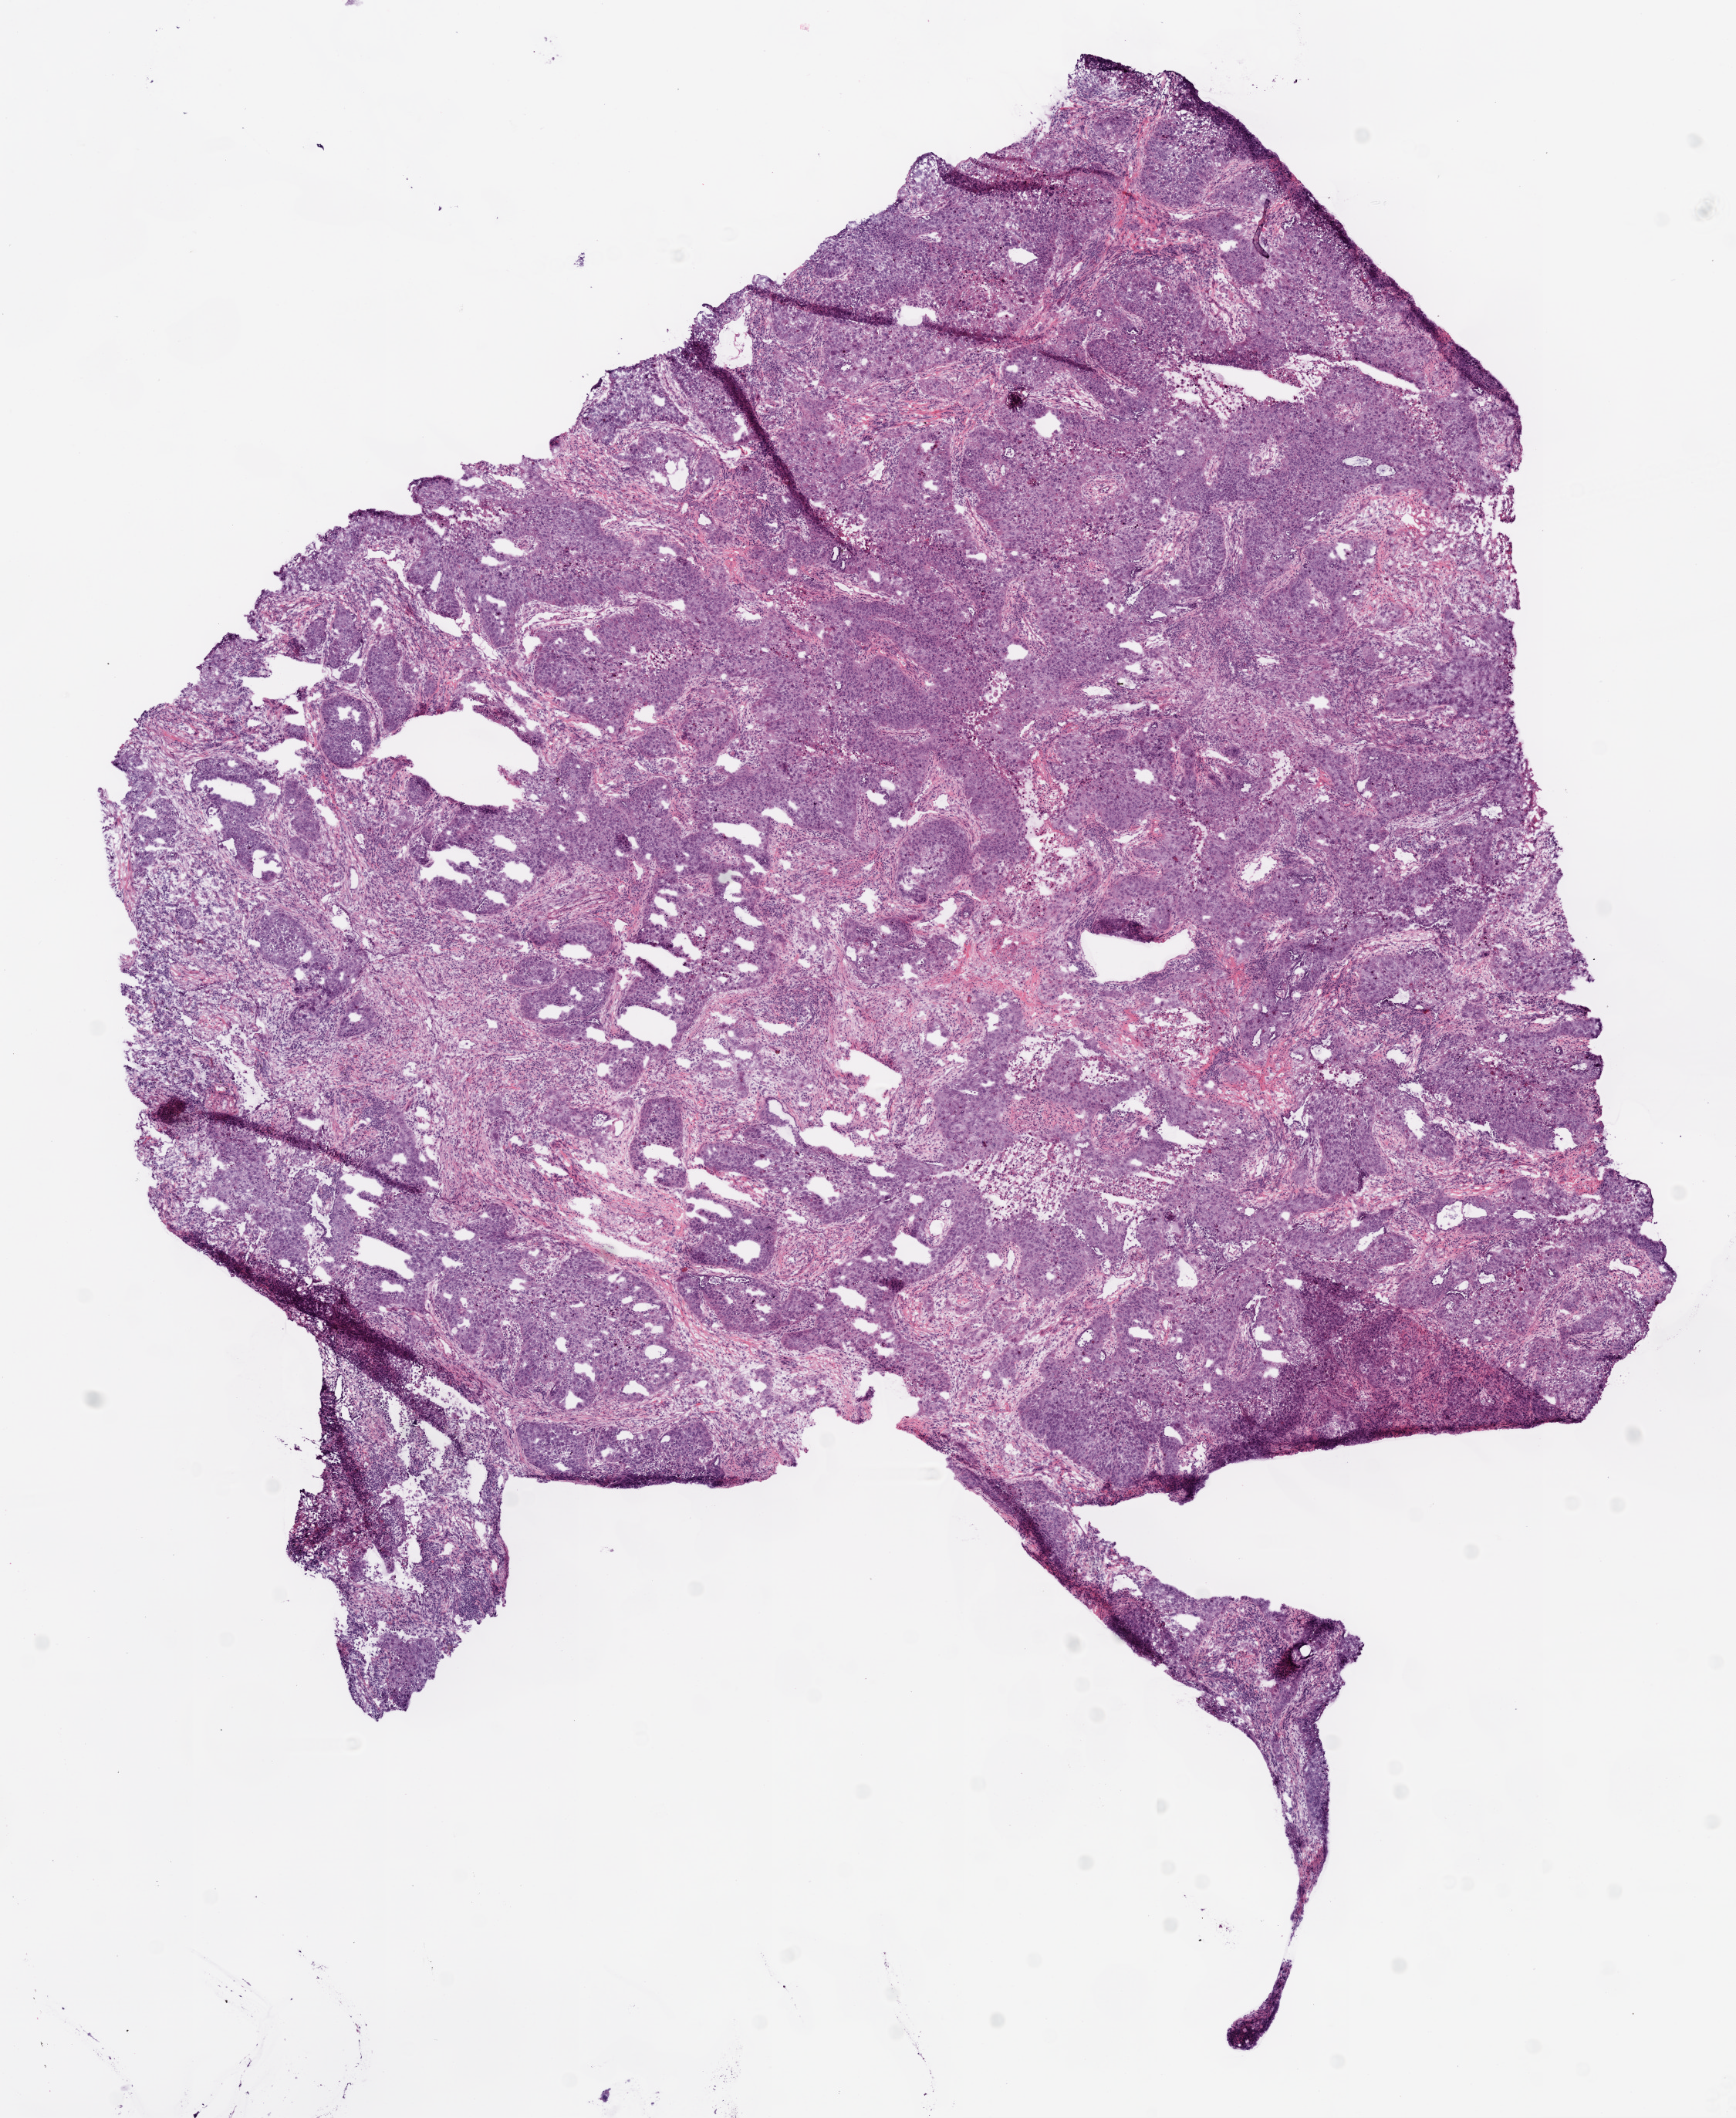
Hematoxylin and eosin (H&E) stained whole-slide image, whole scanned area (about 9.0 x 11.0 mm, from a 20x scan) shown as a low-resolution overview; frozen section from the bottom of the tissue portion; lung, primary tumour sample. Male, age 69 years at initial diagnosis. Composition of this section per pathologist review: tumour cells 80%, tumour nuclei 80%, normal cells 0%, stromal cells 10%, necrosis 10%.
Laterality: left. AJCC pathologic stage: IB (5th edition). Pathologic diagnosis: Squamous cell carcinoma, NOS (lower lobe, lung).